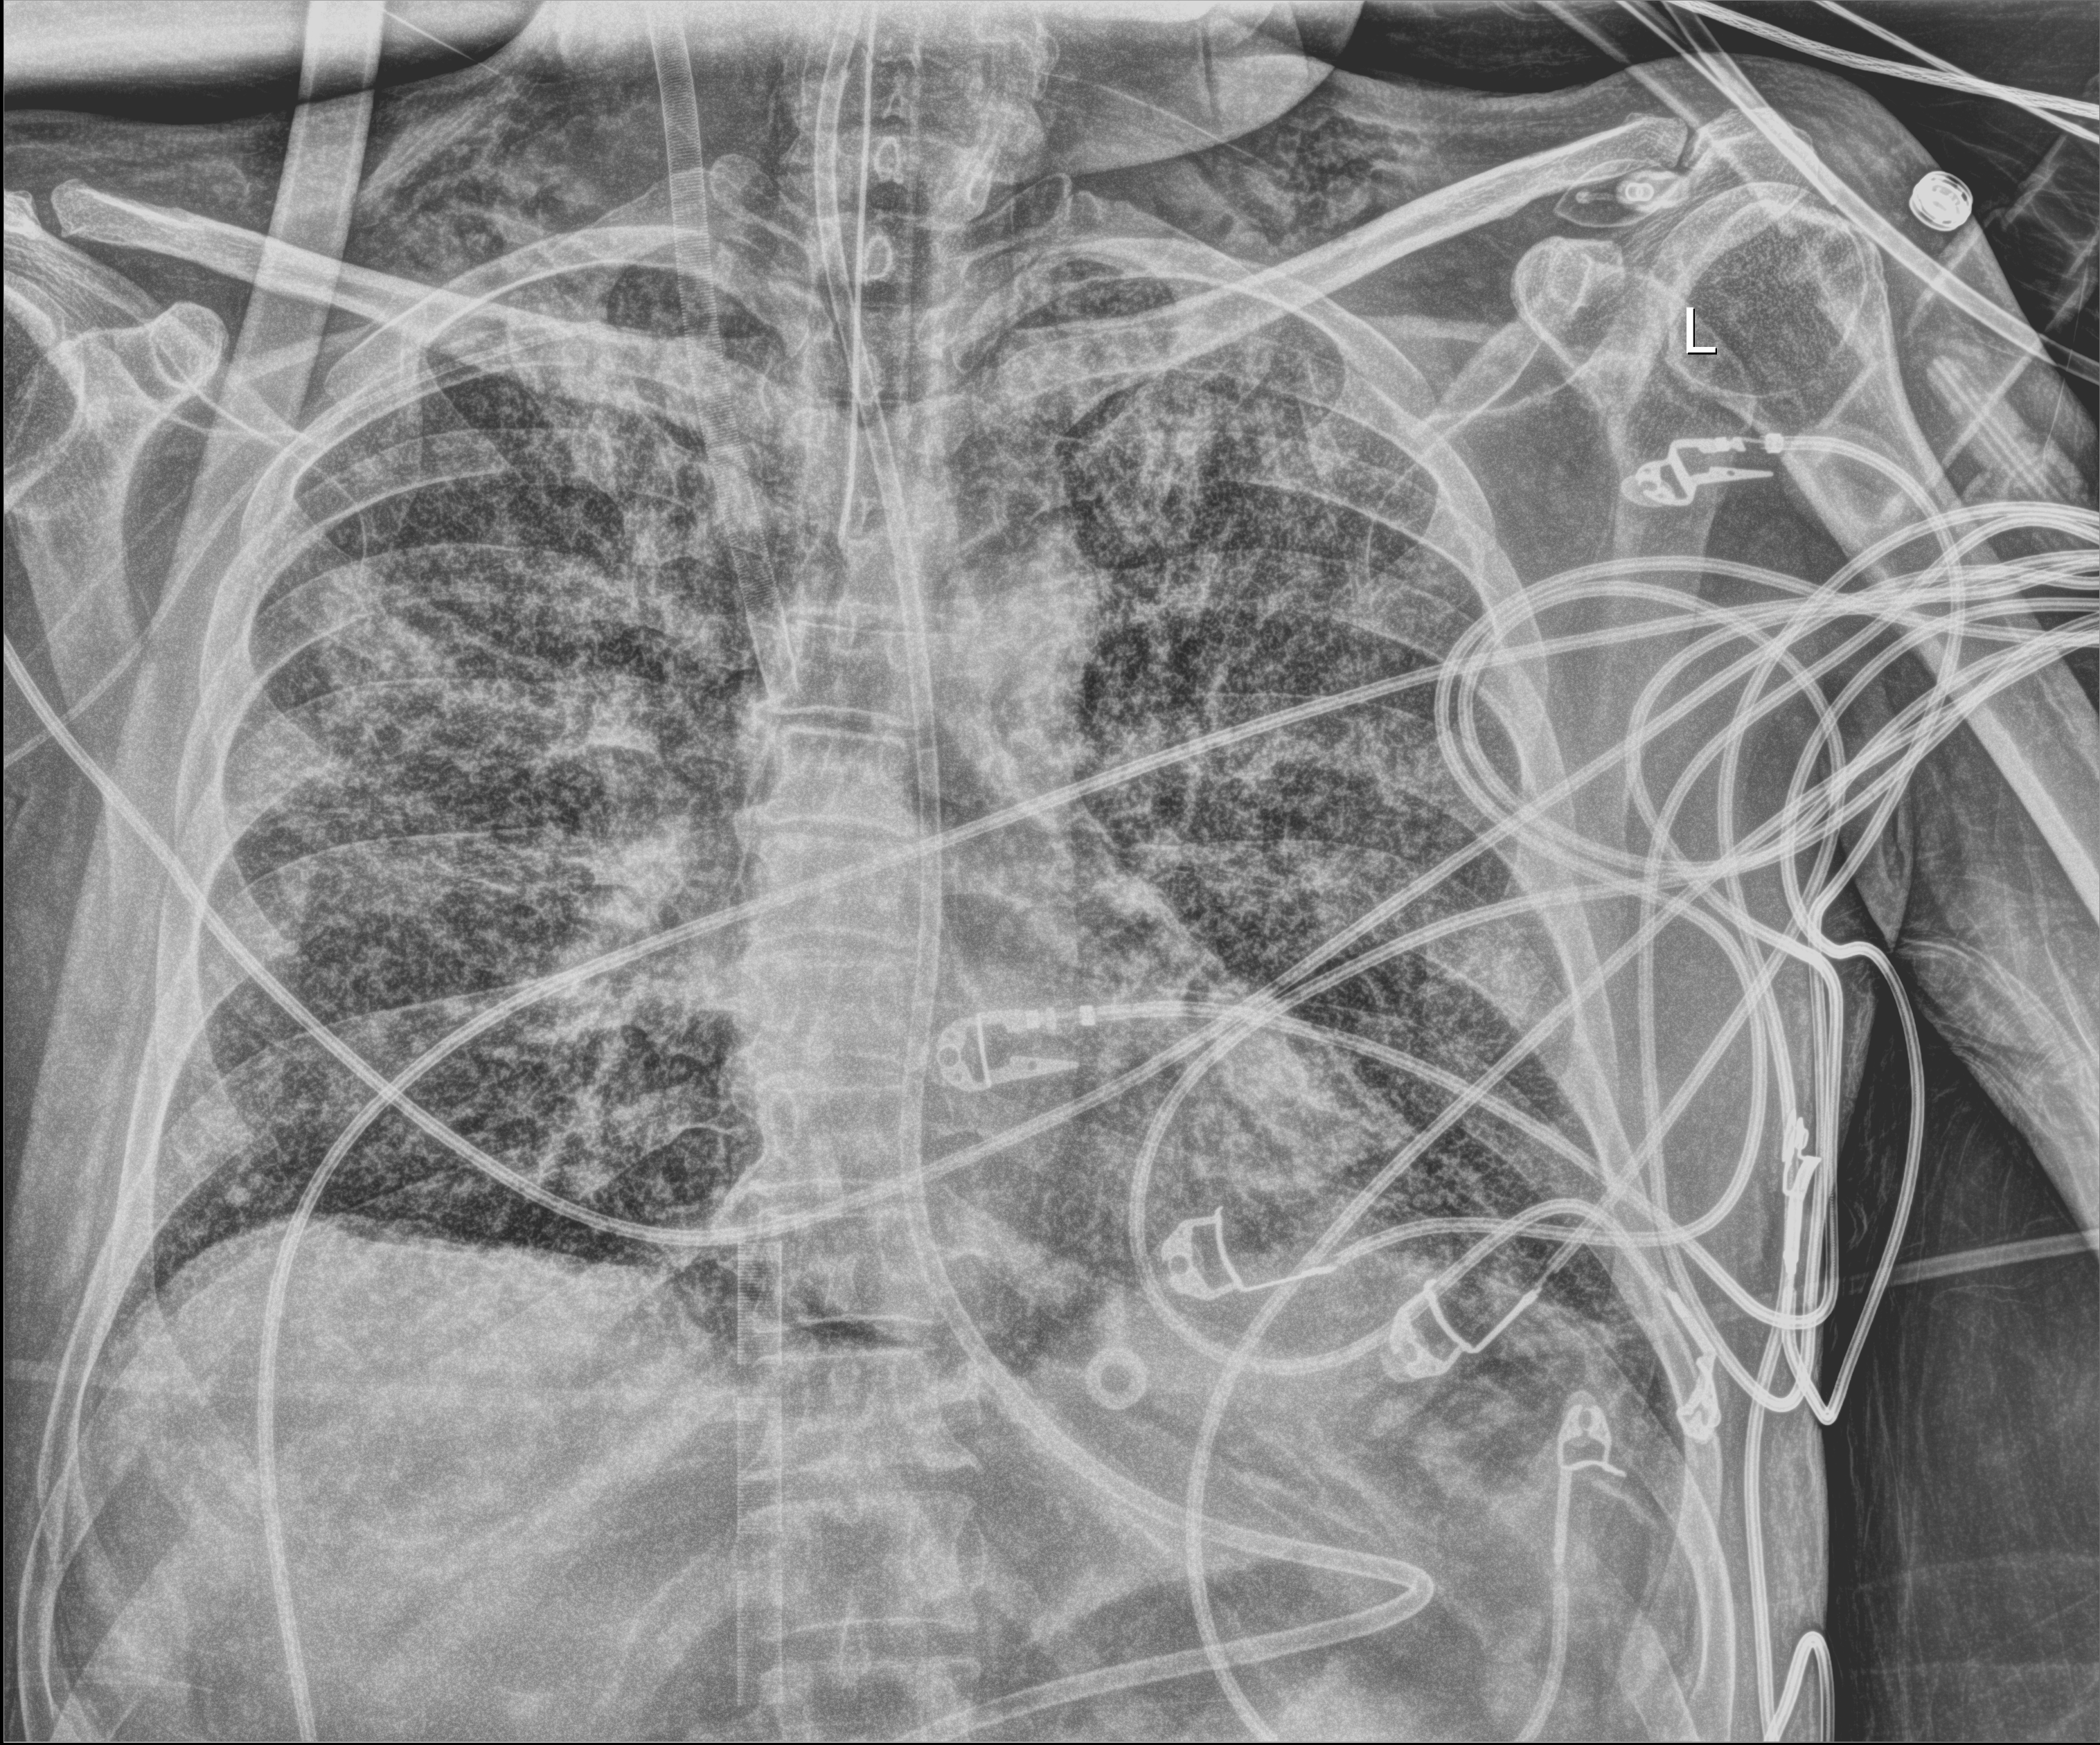
Chest X-ray; anteroposterior (AP) projection. Male patient hospitalised with COVID-19, age 18–59 years.
From the hospital-stay record, not from the radiograph (when in the stay this image was taken is not recorded): length of hospital stay: 42 days.